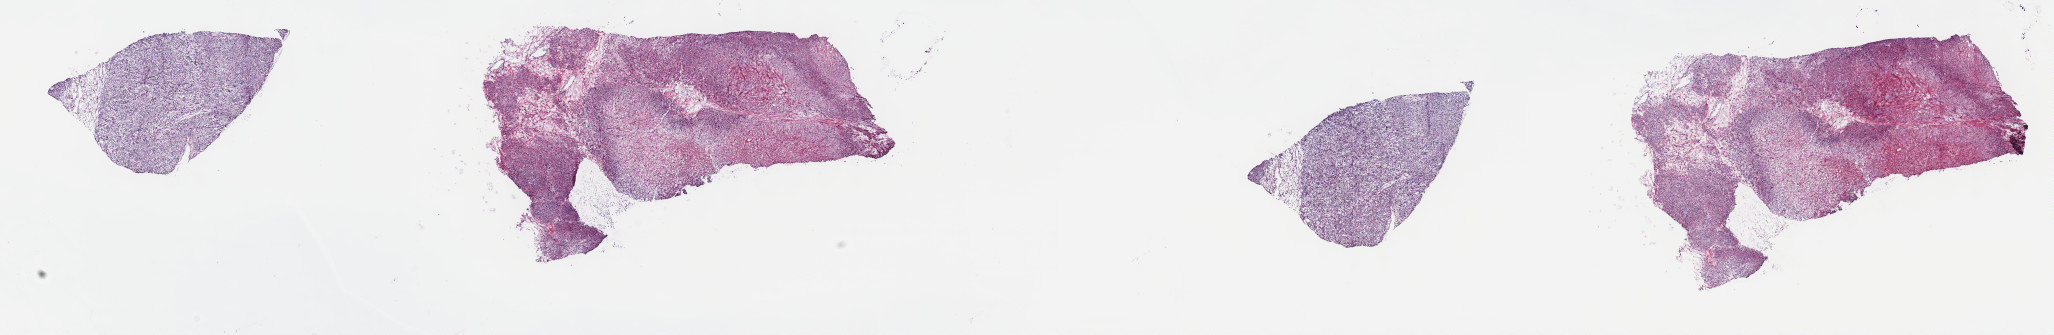
Whole-slide histology image, H&E-stained — a low-resolution overview of the entire scanned area, about 33.2 x 5.4 mm (slide scanned at 40x), frozen section from the top of the tissue portion, primary tumour sample from the retroperitoneum and peritoneum. Patient: female, age at initial diagnosis 57 years. Slide review estimates, as recorded: tumour cells 85%, tumour nuclei 80%, normal cells 0%, stromal cells 0%, necrosis 15%. Infiltration values recorded for this section: lymphocyte infiltration 2%, monocyte infiltration 0%, neutrophil infiltration 0%.
Pathologic diagnosis: Leiomyosarcoma, NOS (retroperitoneum).